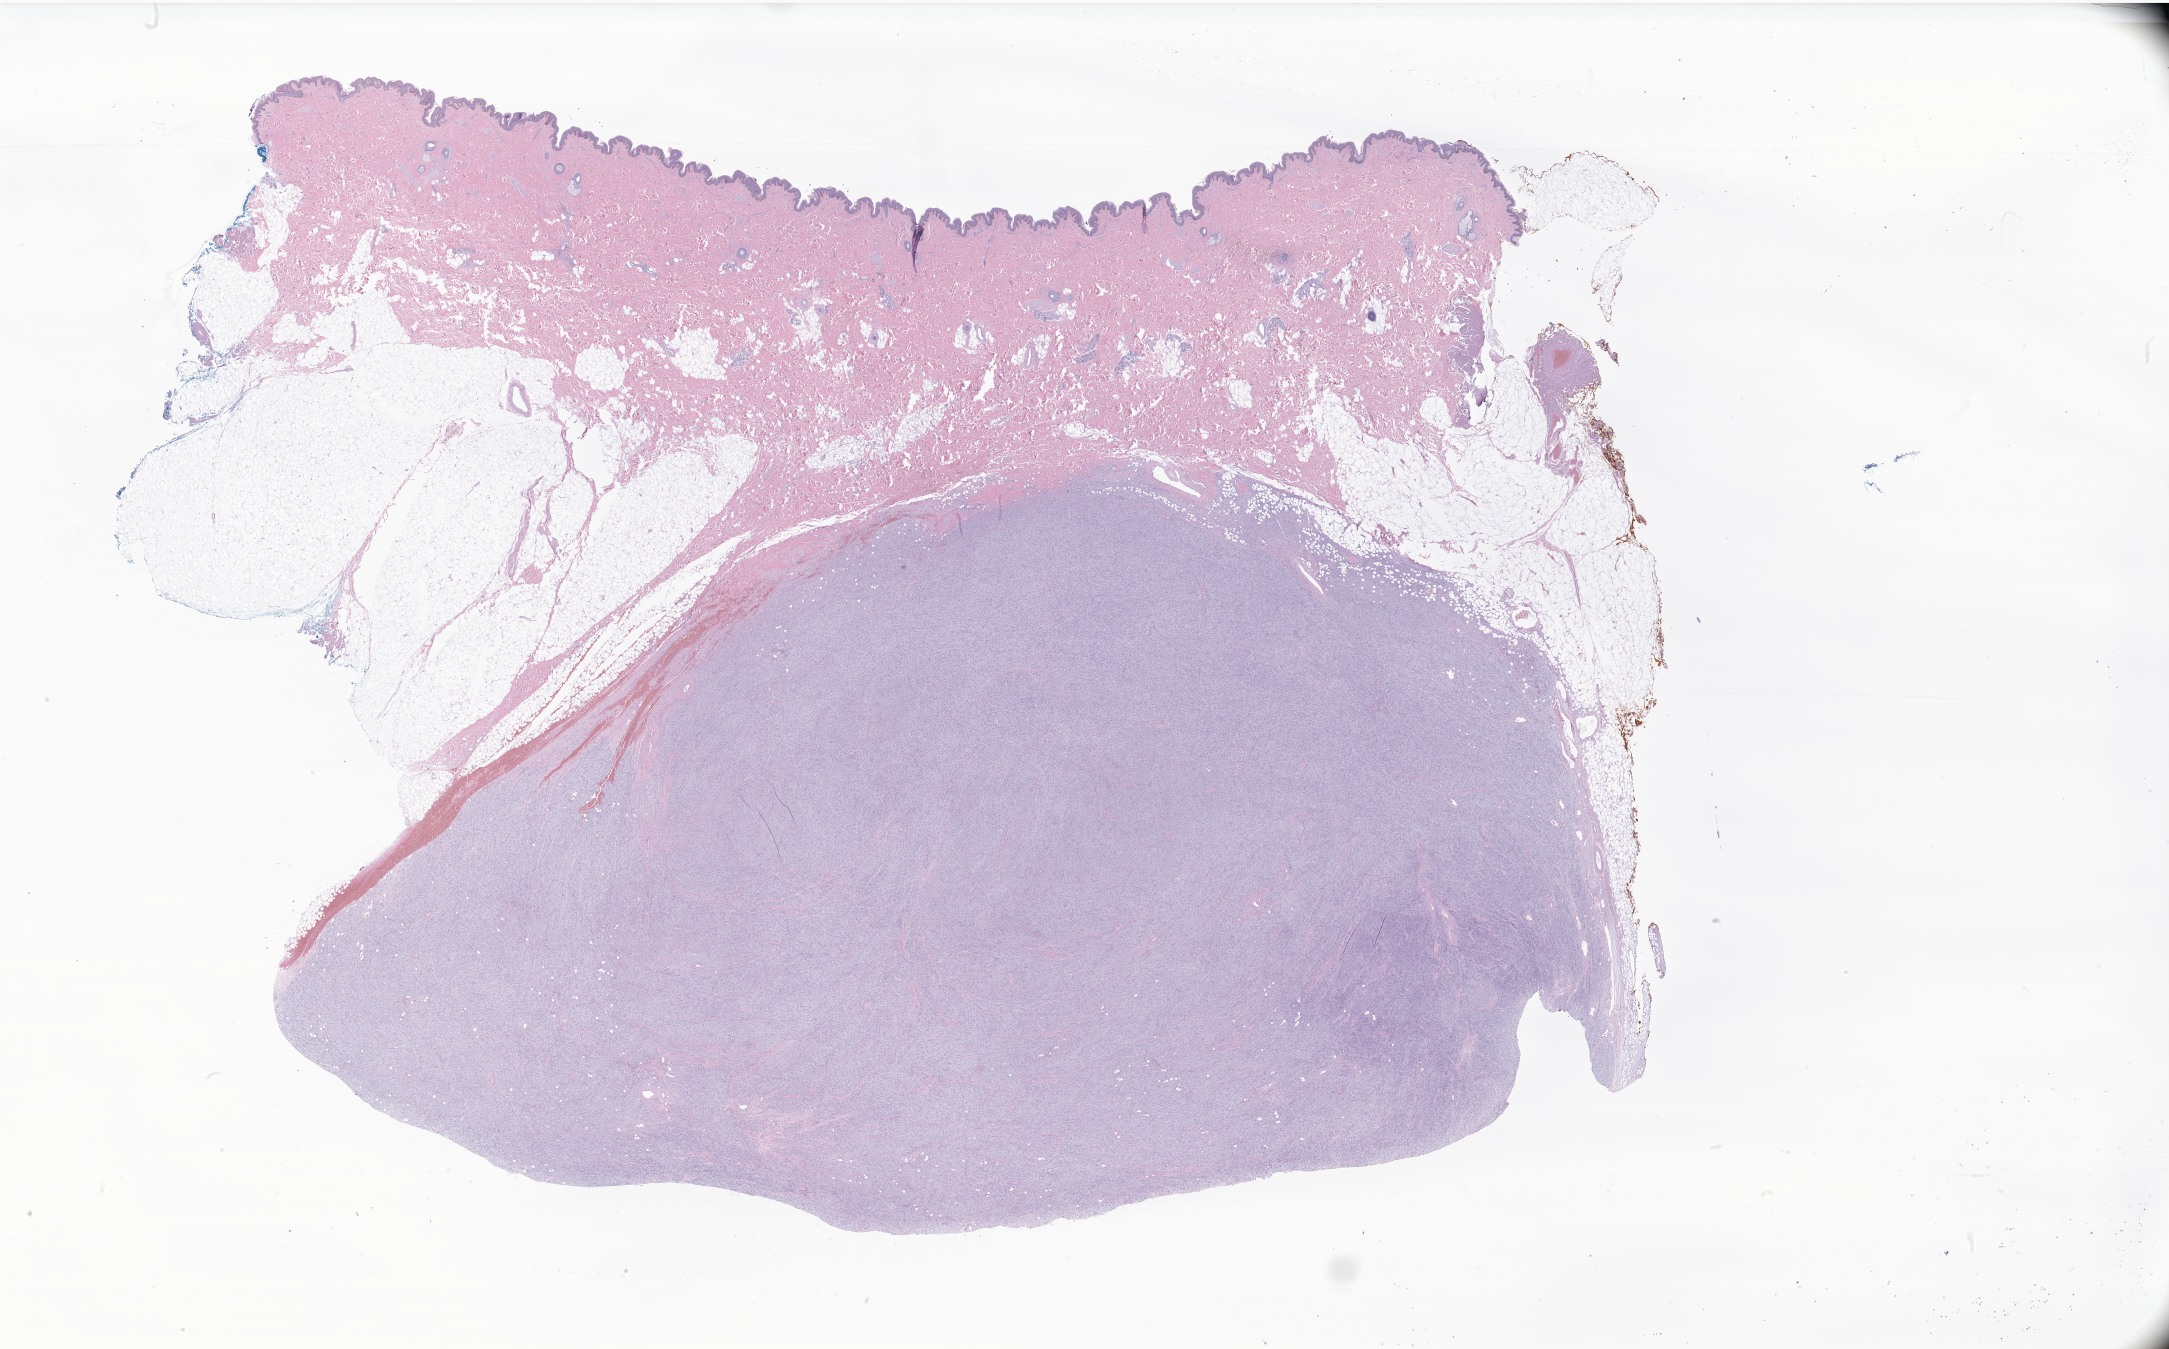
Whole-slide image, H&E stain of tumor tissue from the soft tissue of lower extremity — low-resolution overview of the scanned area, about 36.6 x 22.7 mm. Formalin-fixed paraffin-embedded section. Female patient, age 178 months (14 years 10 months).
Diagnosis (ICD-O-3 morphology term): Dermatofibrosarcoma protuberans, fibrosarcomatous.